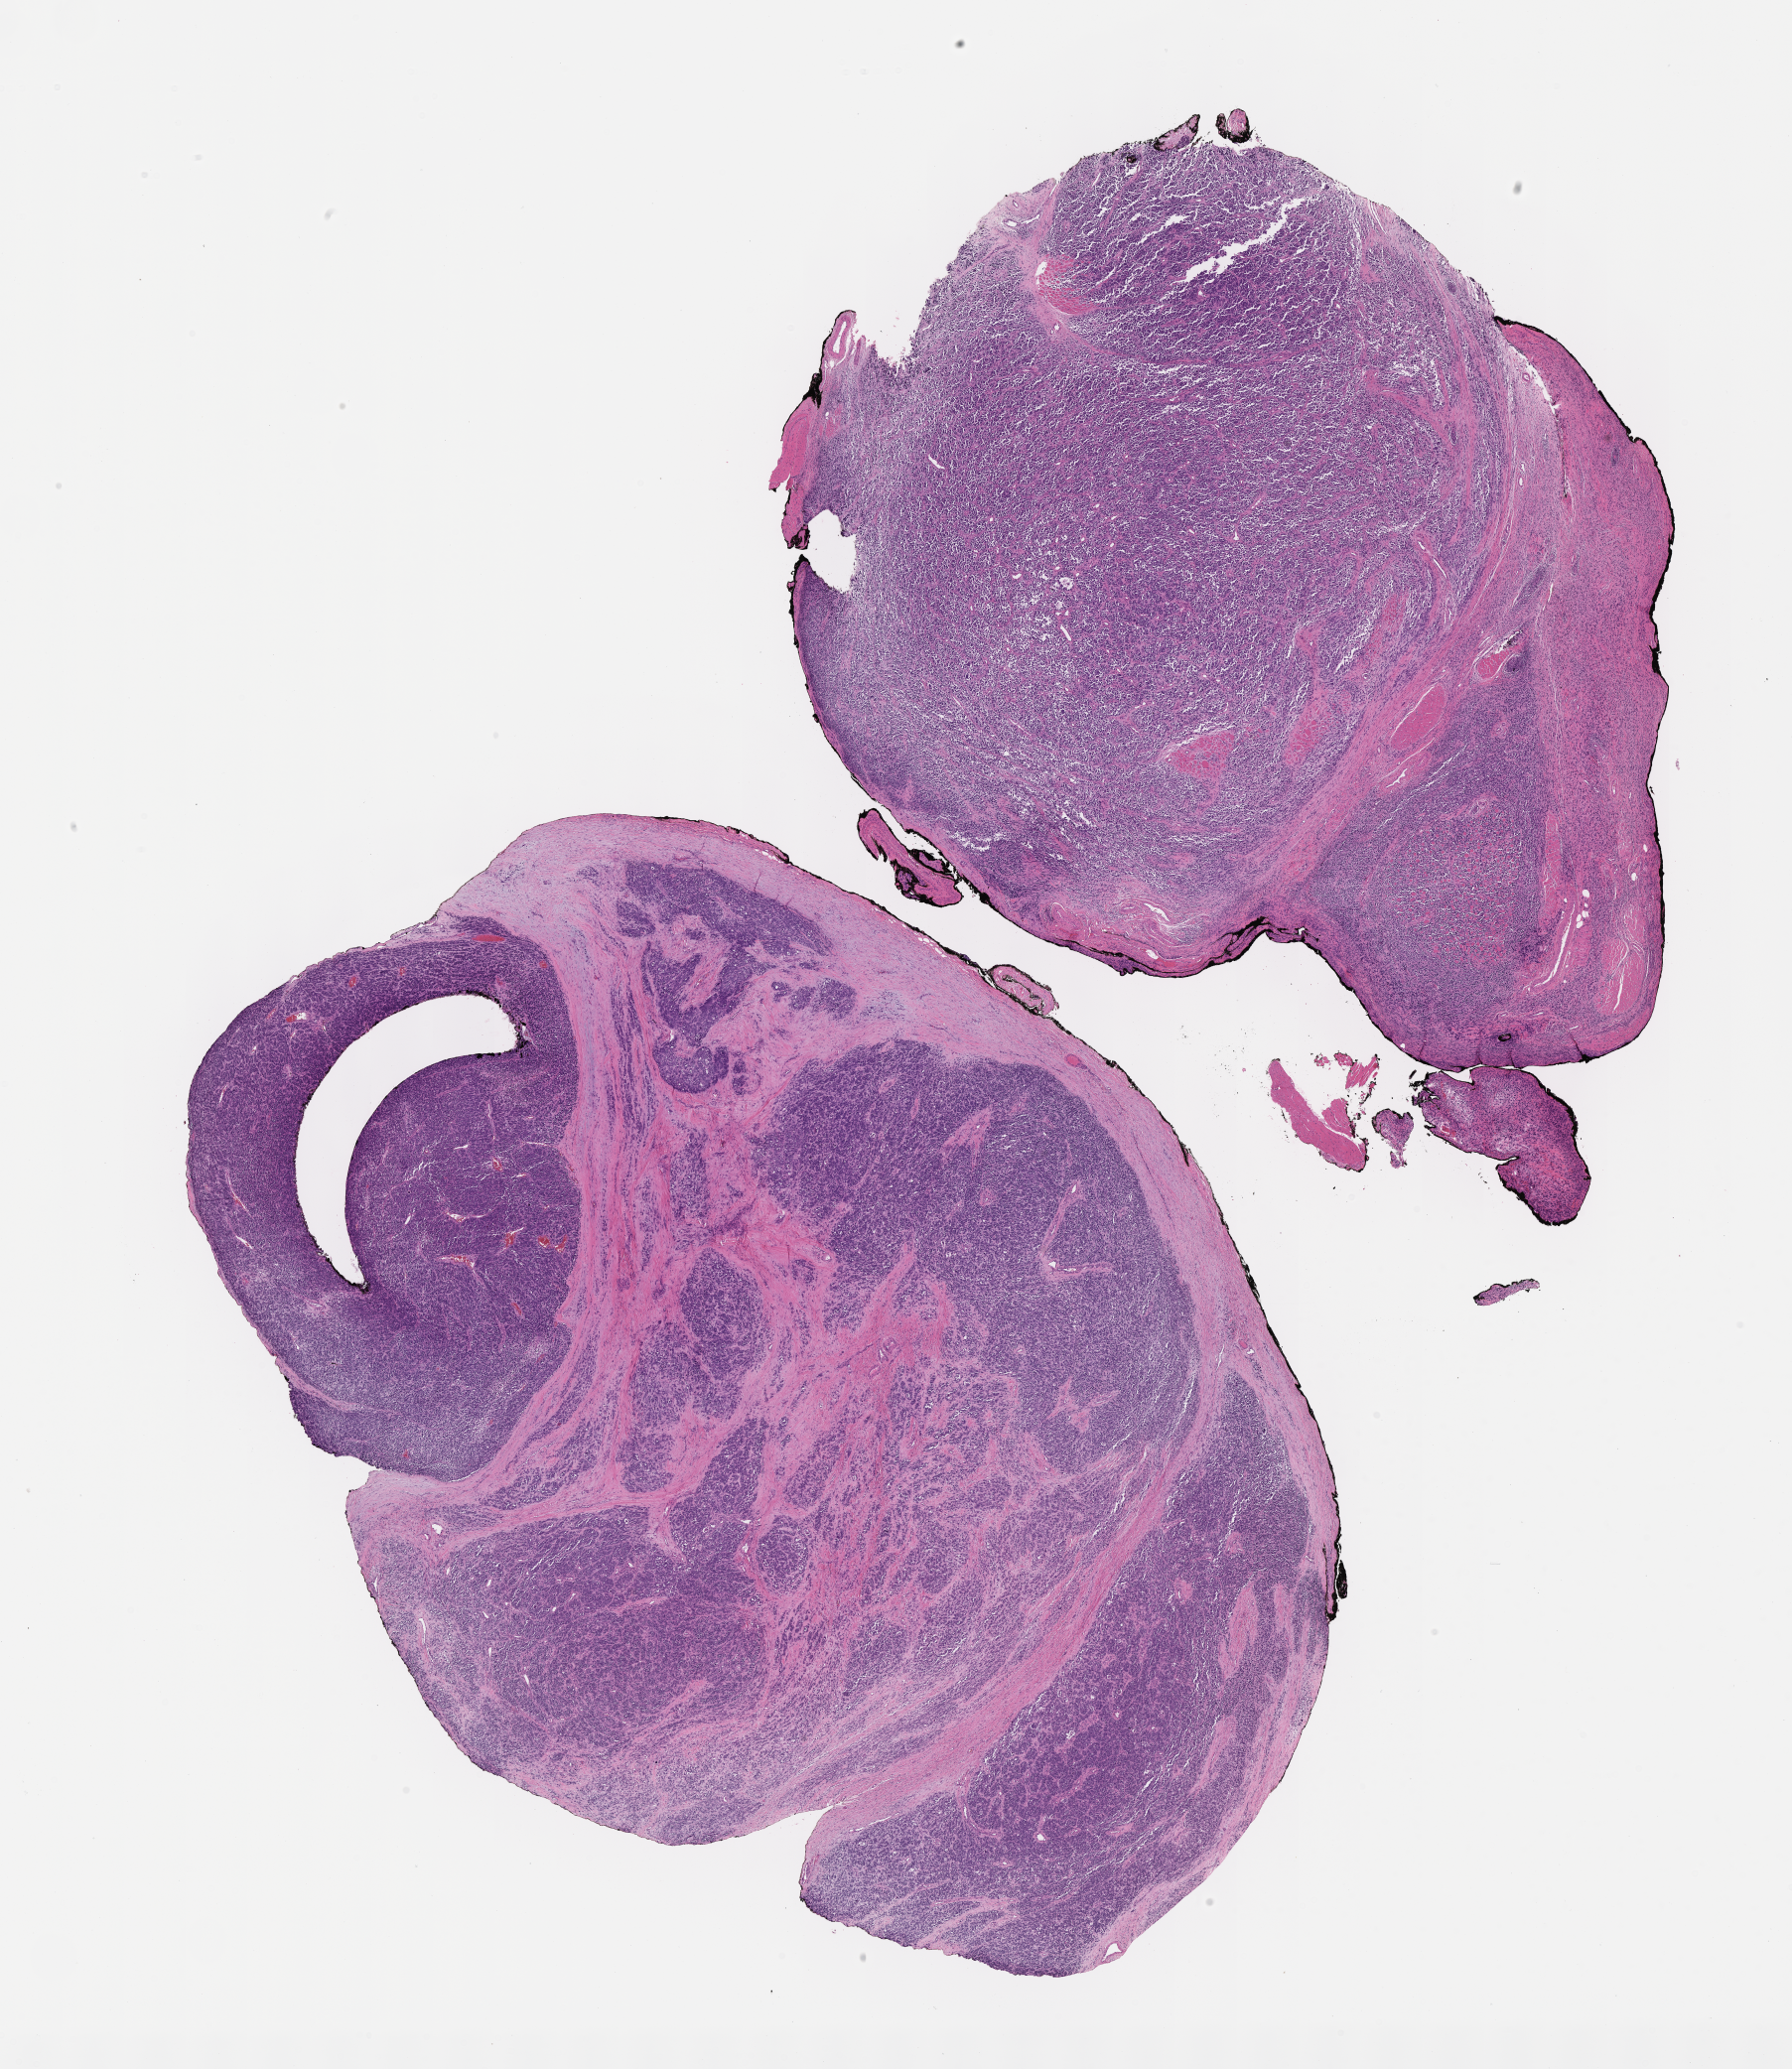
Whole-slide image, haematoxylin and eosin stain of tumor tissue — whole scanned area (about 14.6 x 16.8 mm) shown as a low-resolution overview. Formalin-fixed paraffin-embedded section. Sample anatomic site: paratesticular, right. Male patient, age at diagnosis 7.1 years.
Diagnosis: rhabdomyosarcoma; histological classification: embryonal rhabdomyosarcoma. Stage (as recorded): 1.